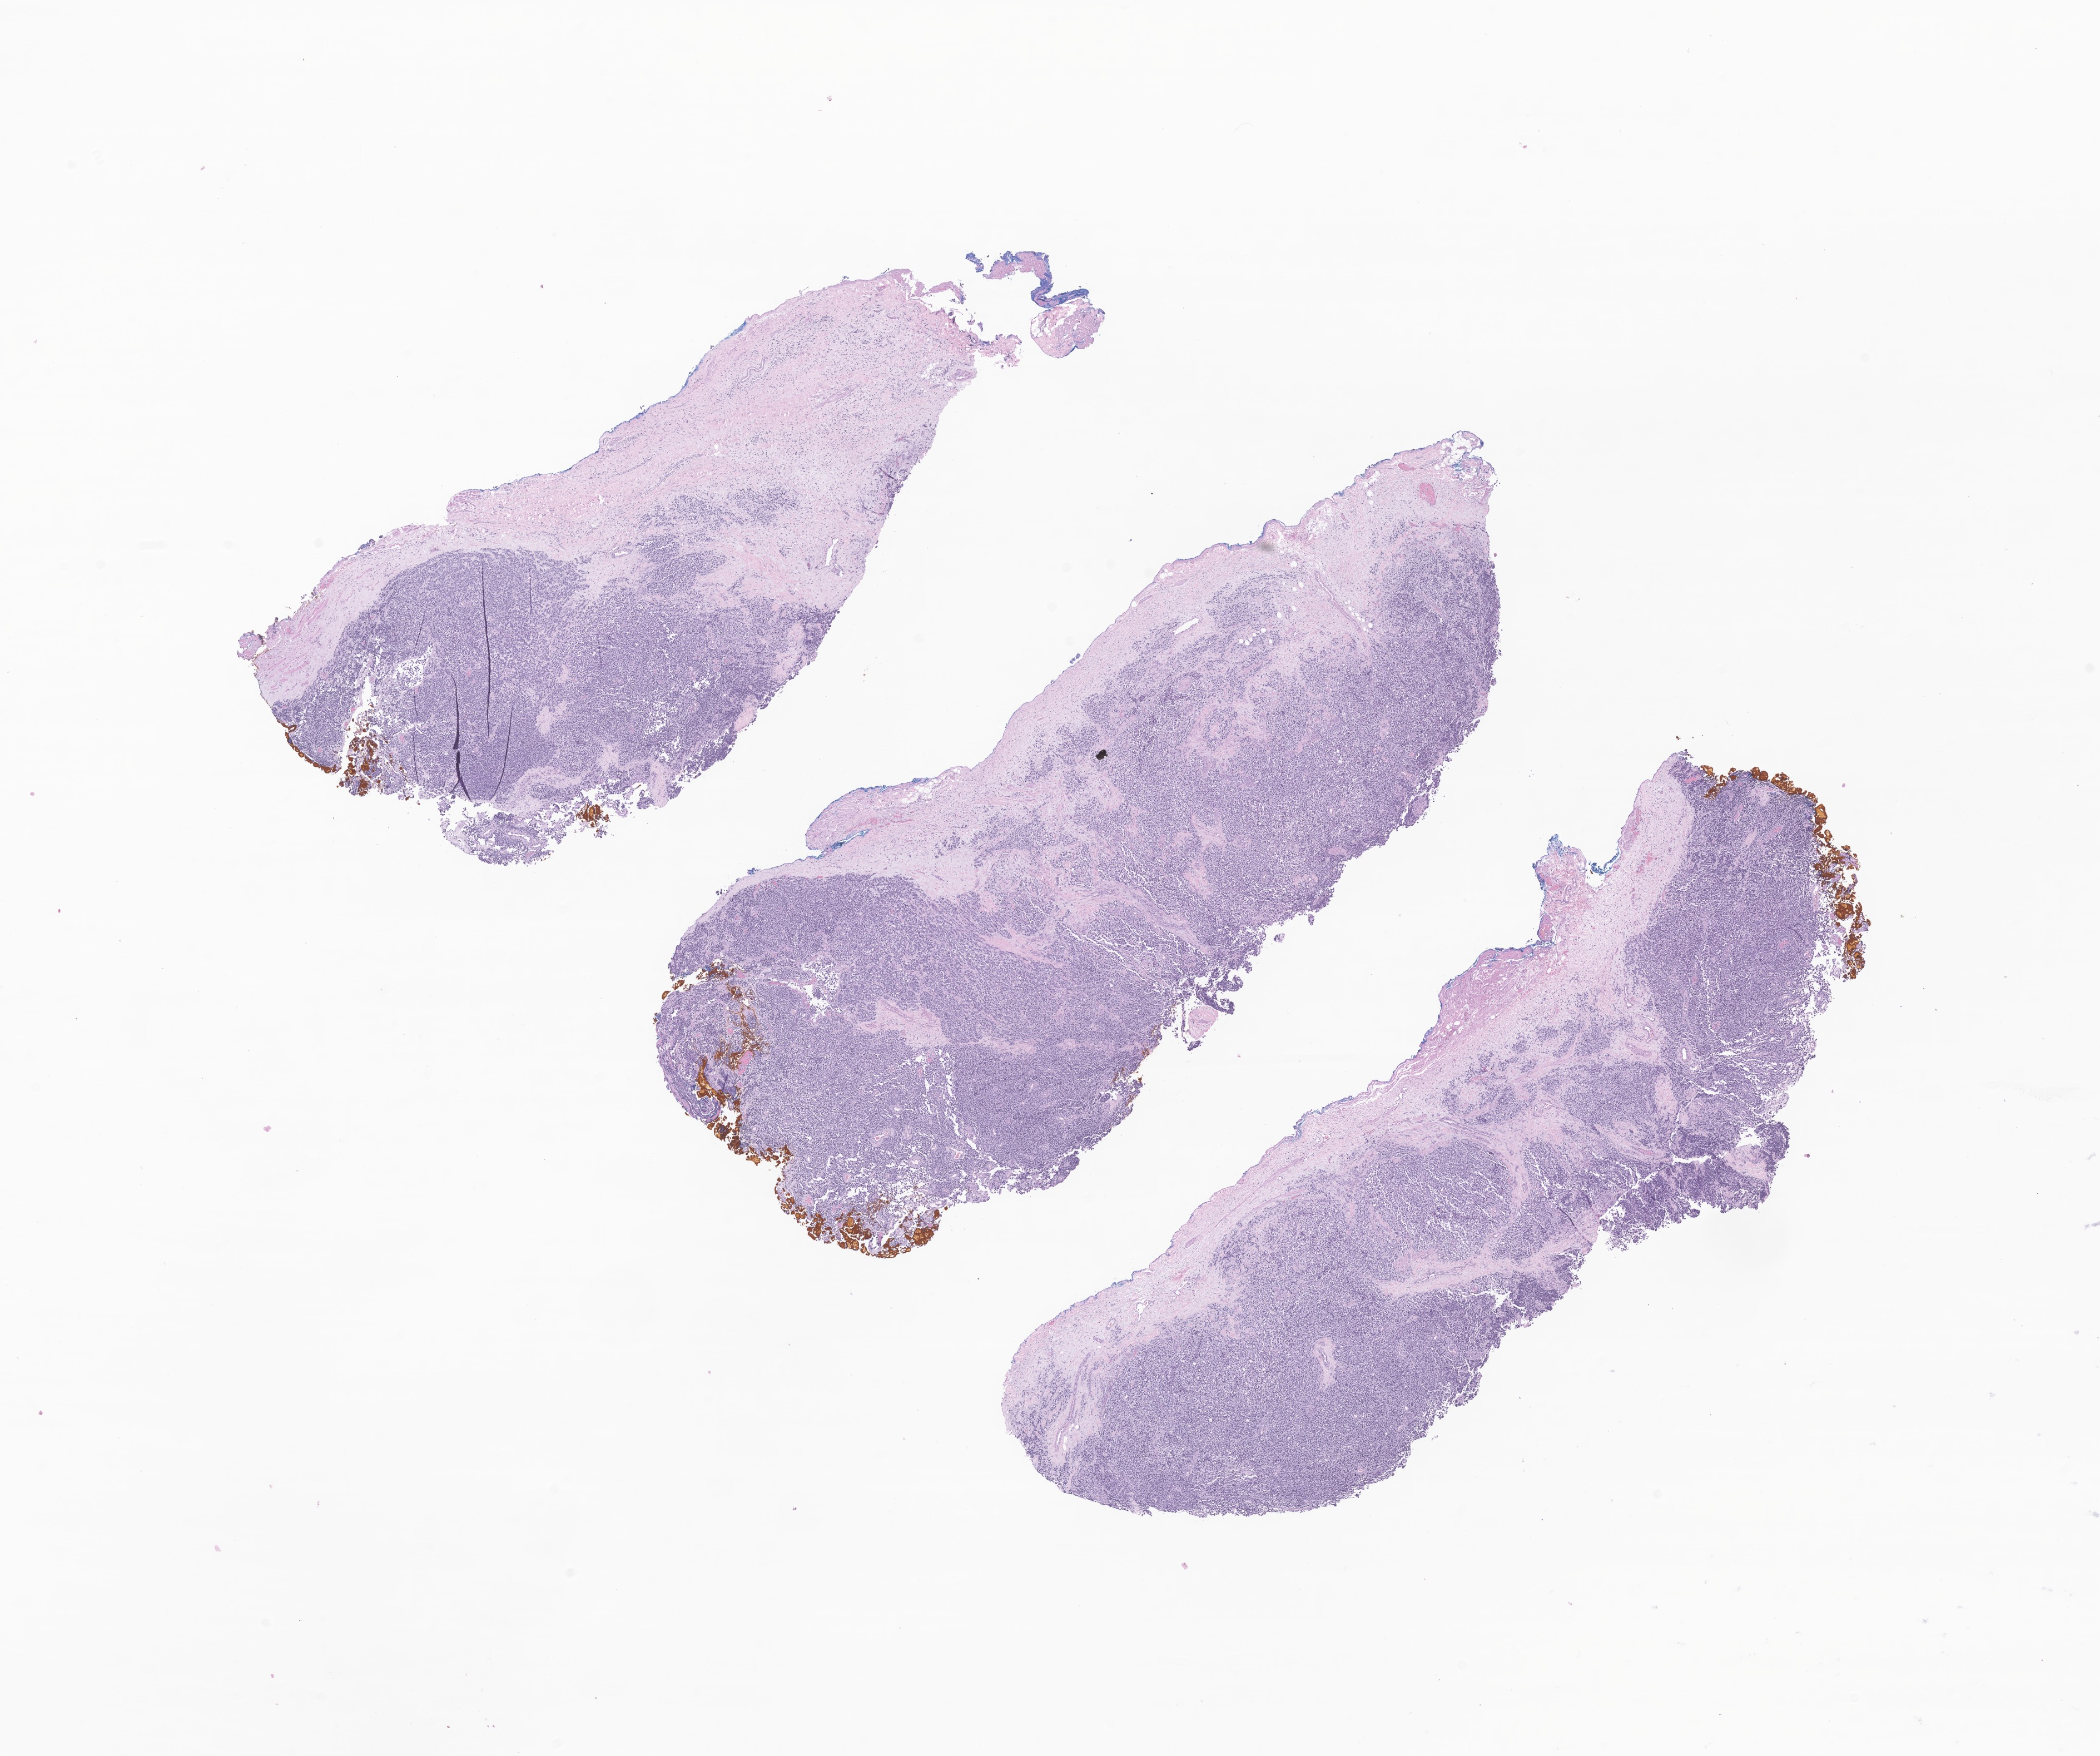
Hematoxylin and eosin (H&E) whole-slide image of tumor tissue from the orbit, shown as a low-resolution overview of the whole scanned area (about 15.9 x 13.3 mm); formalin-fixed paraffin-embedded section. Patient male; age 52 months (4 years 4 months).
Diagnosis (ICD-O-3 morphology term): Rhabdomyosarcoma, NOS.